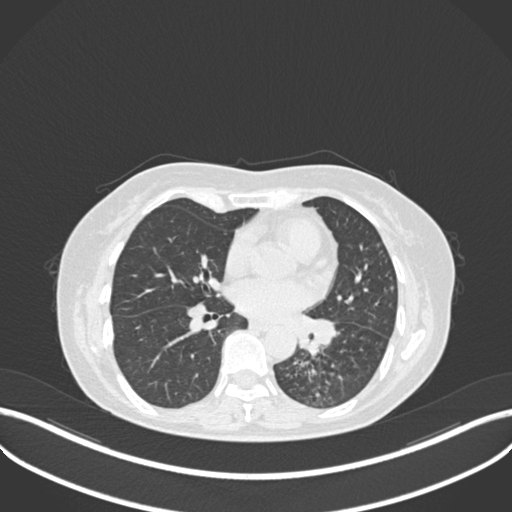
Chest CT, one axial slice; position 122 of 270 along the scan axis; lung window (W 1500 / L -600 HU); 1 mm slice thickness; 512 × 512 image matrix. Patient: female, 63 years. From the clinical record (not read from this slice): clinical TNM (as recorded): T1b N0 M0; histopathological grade: G2-3.
Structures marked on this image (rectangle marked by the reading radiologist):
- lung tumour (recorded histology: adenocarcinoma): bounding box (x1, y1, x2, y2) in pixels: (293, 314, 336, 356)